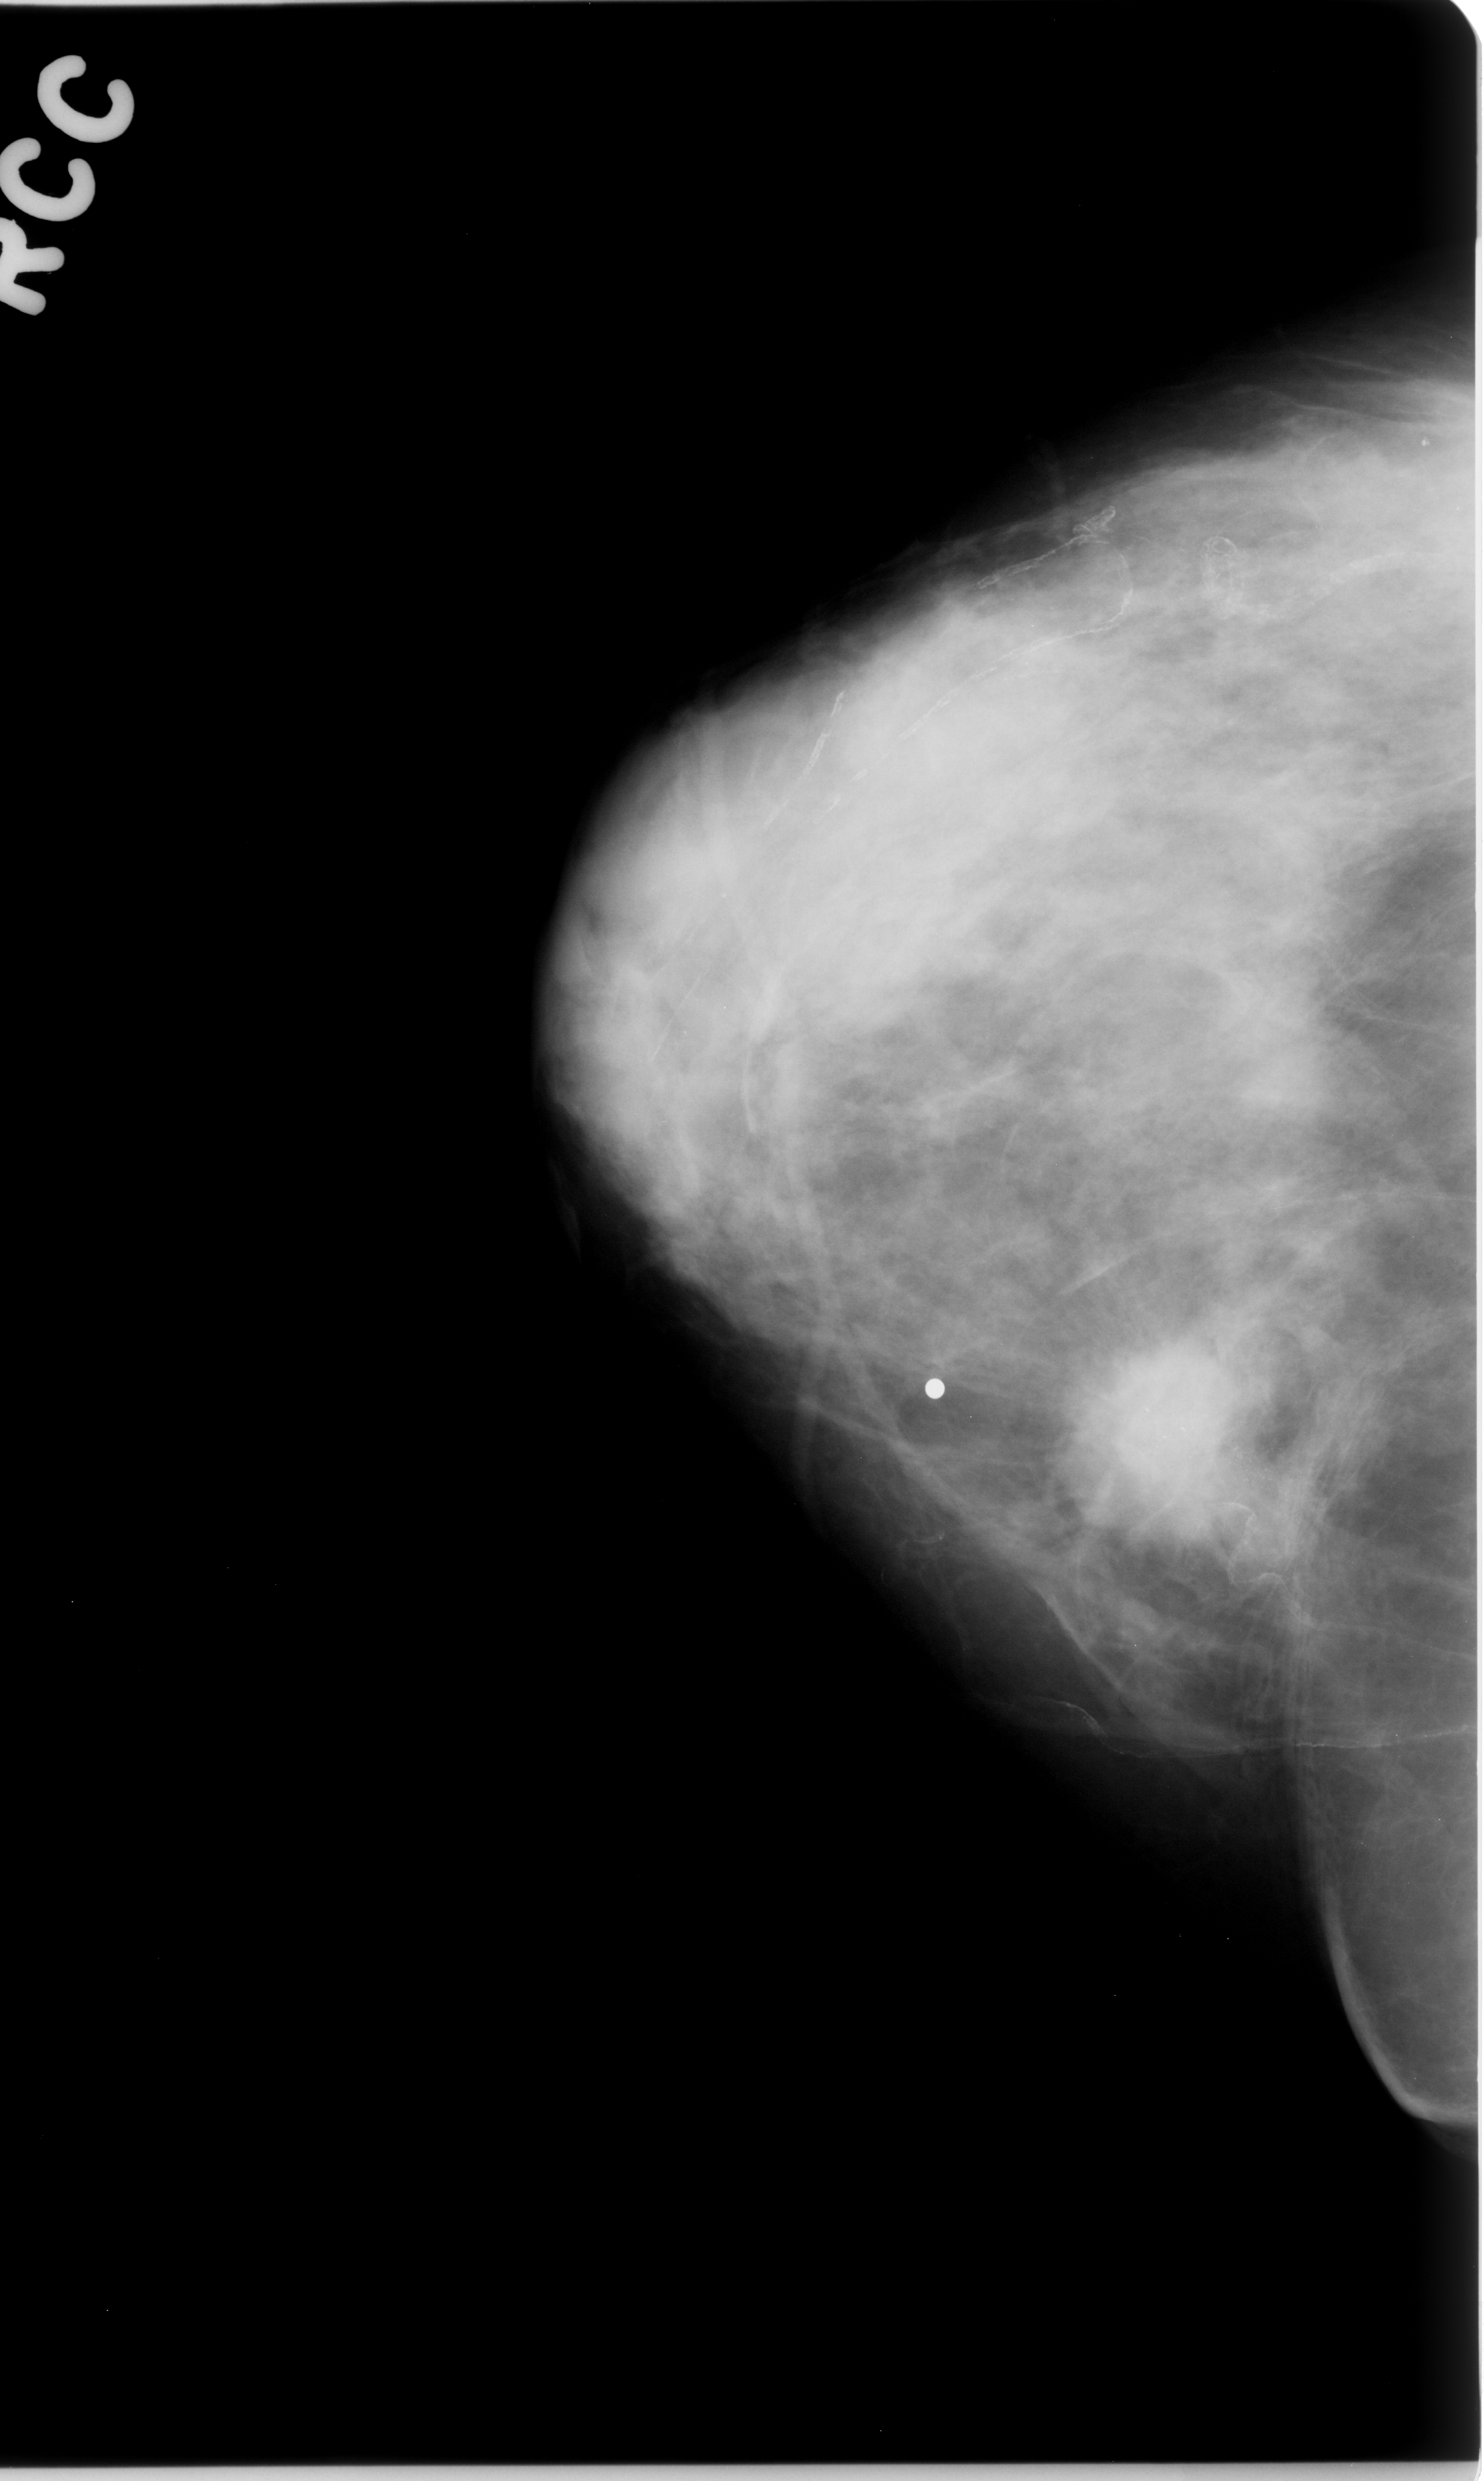
Digitized screen-film mammogram; right breast; CC view; BI-RADS breast density category 3 (scale 1–4); 1484 × 2481 image matrix.
Expert-marked regions of interest on this image (one box per marked abnormality):
- calcifications, morphology amorphous, distribution clustered; BI-RADS assessment category 5; pathology result (as recorded, not read from the image): malignant: box from (x=966, y=1189) to (x=1434, y=1669) px